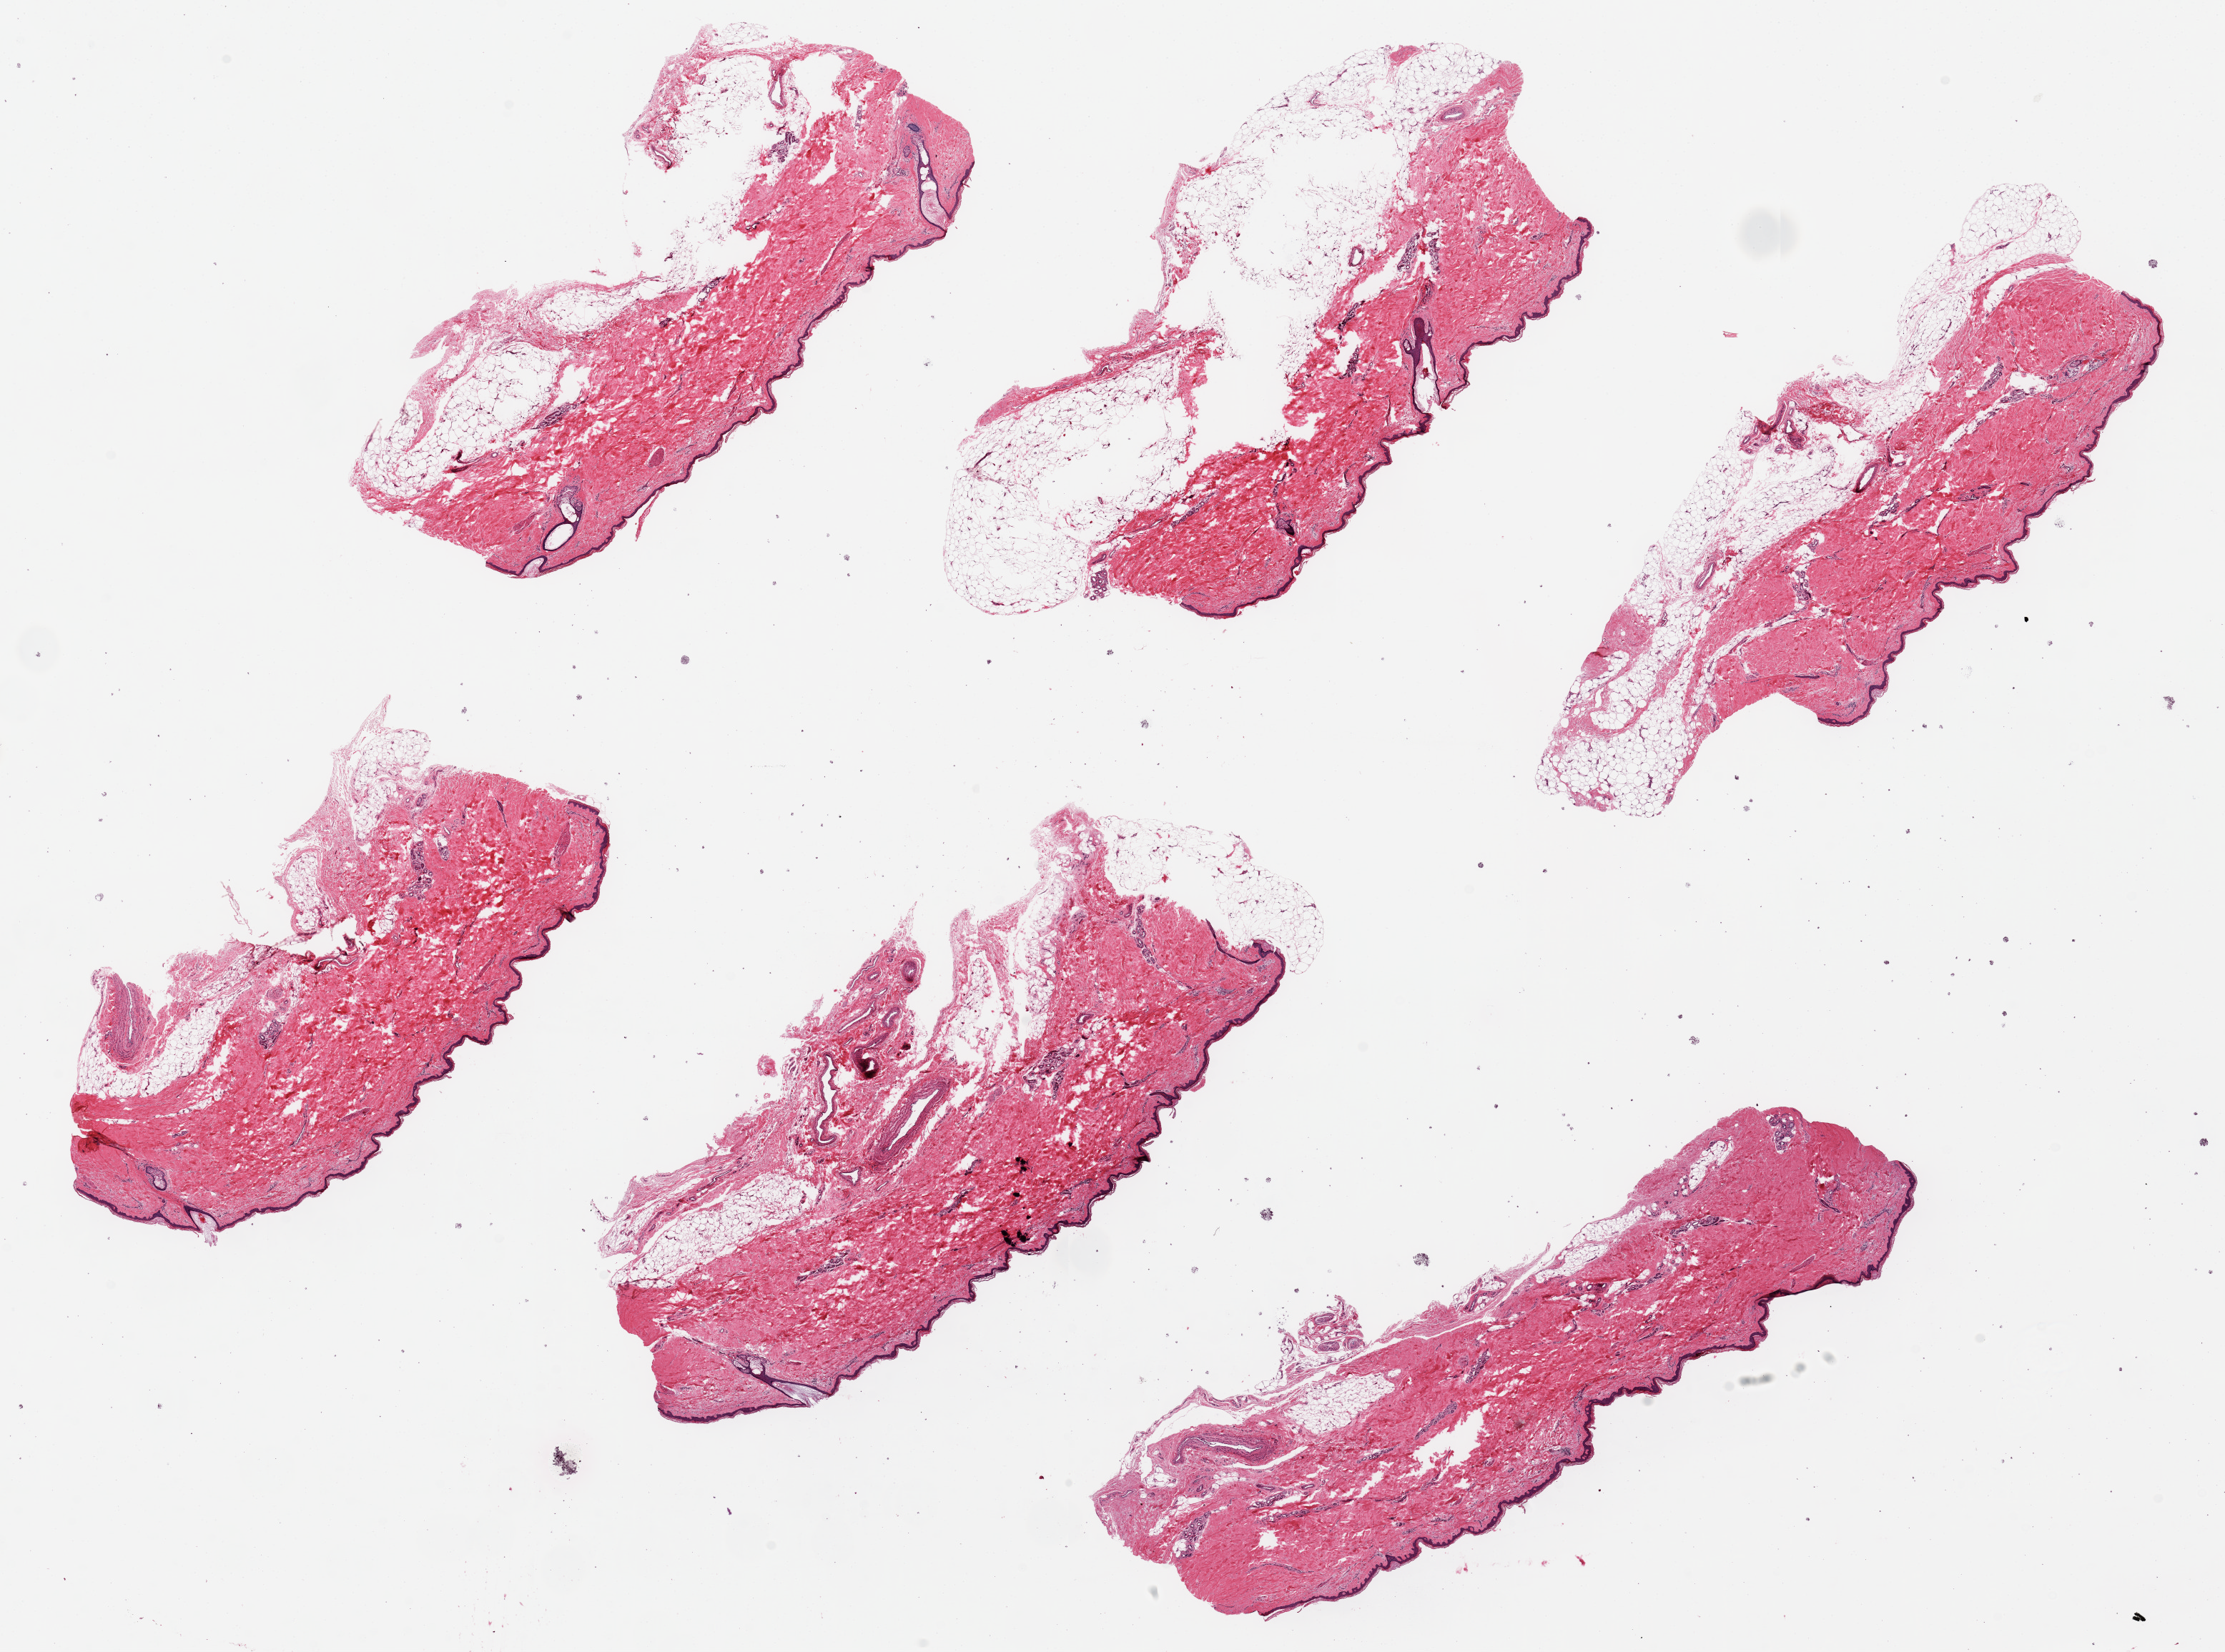
Whole-slide image, H&E stain — low-resolution overview of the scanned area, about 24.6 x 18.3 mm (slide scanned at 20x); PAXgene-fixed, paraffin-embedded tissue; section of skin of lower leg (target tissue); donor tissue sample. Donor sex: male.
Reviewer comment on this tissue sample: 6 ~8x3mm pieces. Squamous epithelium is ~1-2% of thickness. ~1mm layer of subcutaneous fat present in 5 pieces.